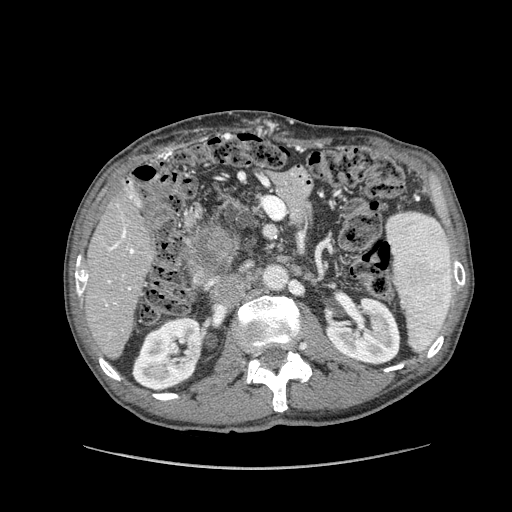
Contrast-enhanced abdominal CT (liver protocol), one axial slice. Position 43 of 162 along the scan axis. Reconstruction kernel STANDARD. Soft-tissue window (W 400 / L 40 HU). 512 × 512 image matrix, field of view 400 × 400 mm. From the clinical record (not read from this slice): diagnosis: hepatocellular carcinoma (patient treated with transarterial chemoembolisation; whether this scan precedes or follows treatment is not stated here); TNM stage (as recorded): Stage-IIIA; Child-Pugh class: A; tumour nodularity: multinodular; tumour size: 9.9 cm.
Outlined on this slice (semi-automatically segmented with operator editing):
- liver parenchyma outside the tumour (the mass and vessels are separate outlines, so this box may not span the whole liver): bounding box [x1, y1, x2, y2] px = [82, 181, 156, 358]
- mass: [187, 226, 230, 279]
- liver vessels: [84, 183, 140, 306]